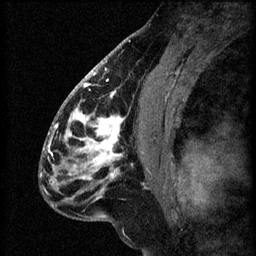
Breast MRI (dynamic contrast-enhanced), one sagittal slice. Slice 34 of 60 in the series (ordered by position). 3 images stored at this slice position (order not interpretable as contrast timing). 1.5 T. TE 4.2 ms, TR 8.2 ms. 2.2 mm slice thickness. 256 × 256 image matrix, field of view 180 × 180 mm. Female patient, age 41 years.
Structures marked on this image (semi-automatic segmentation, software-assisted and operator-edited):
- analysis volume of interest (the breast-tissue region the enhancement analysis was run in; not a lesion): bounding box (x1, y1, x2, y2) in pixels: (56, 104, 157, 207)
- tumour enhancement mask (voxels above the 70 % enhancement threshold inside the analysis volume of interest): (56, 104, 126, 201)